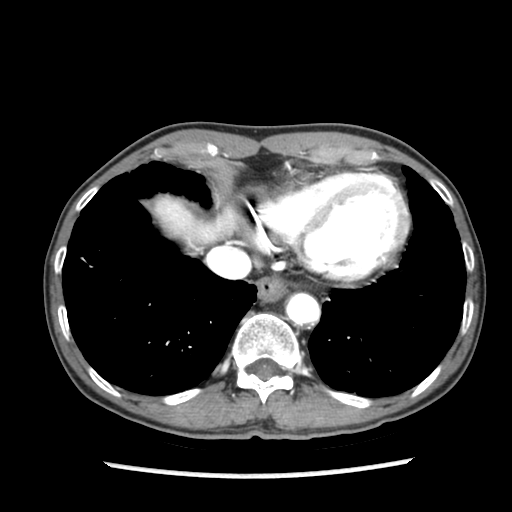
Contrast-enhanced abdominal CT (liver protocol), one axial slice. Position 75 of 87 along the scan axis. Reconstruction kernel STANDARD. 140 kVp. Soft-tissue window (W 400 / L 40 HU). 2.5 mm slice thickness. 512 × 512 image matrix, field of view 300 × 300 mm. Case-level facts recorded for this patient, not image findings: diagnosis: hepatocellular carcinoma (patient treated with transarterial chemoembolisation; whether this scan precedes or follows treatment is not stated here); TNM stage (as recorded): Stage-IIIB; Child-Pugh class: A; tumour differentiation: well differentiated; tumour nodularity: uninodular.
Annotated regions visible in this slice (semi-automatic segmentation, software-assisted and operator-edited):
- abdominal aorta: bounding box [x1, y1, x2, y2] px = [288, 296, 319, 325]
- liver parenchyma outside the tumour (the mass and vessels are separate outlines, so this box may not span the whole liver): [154, 196, 238, 244]